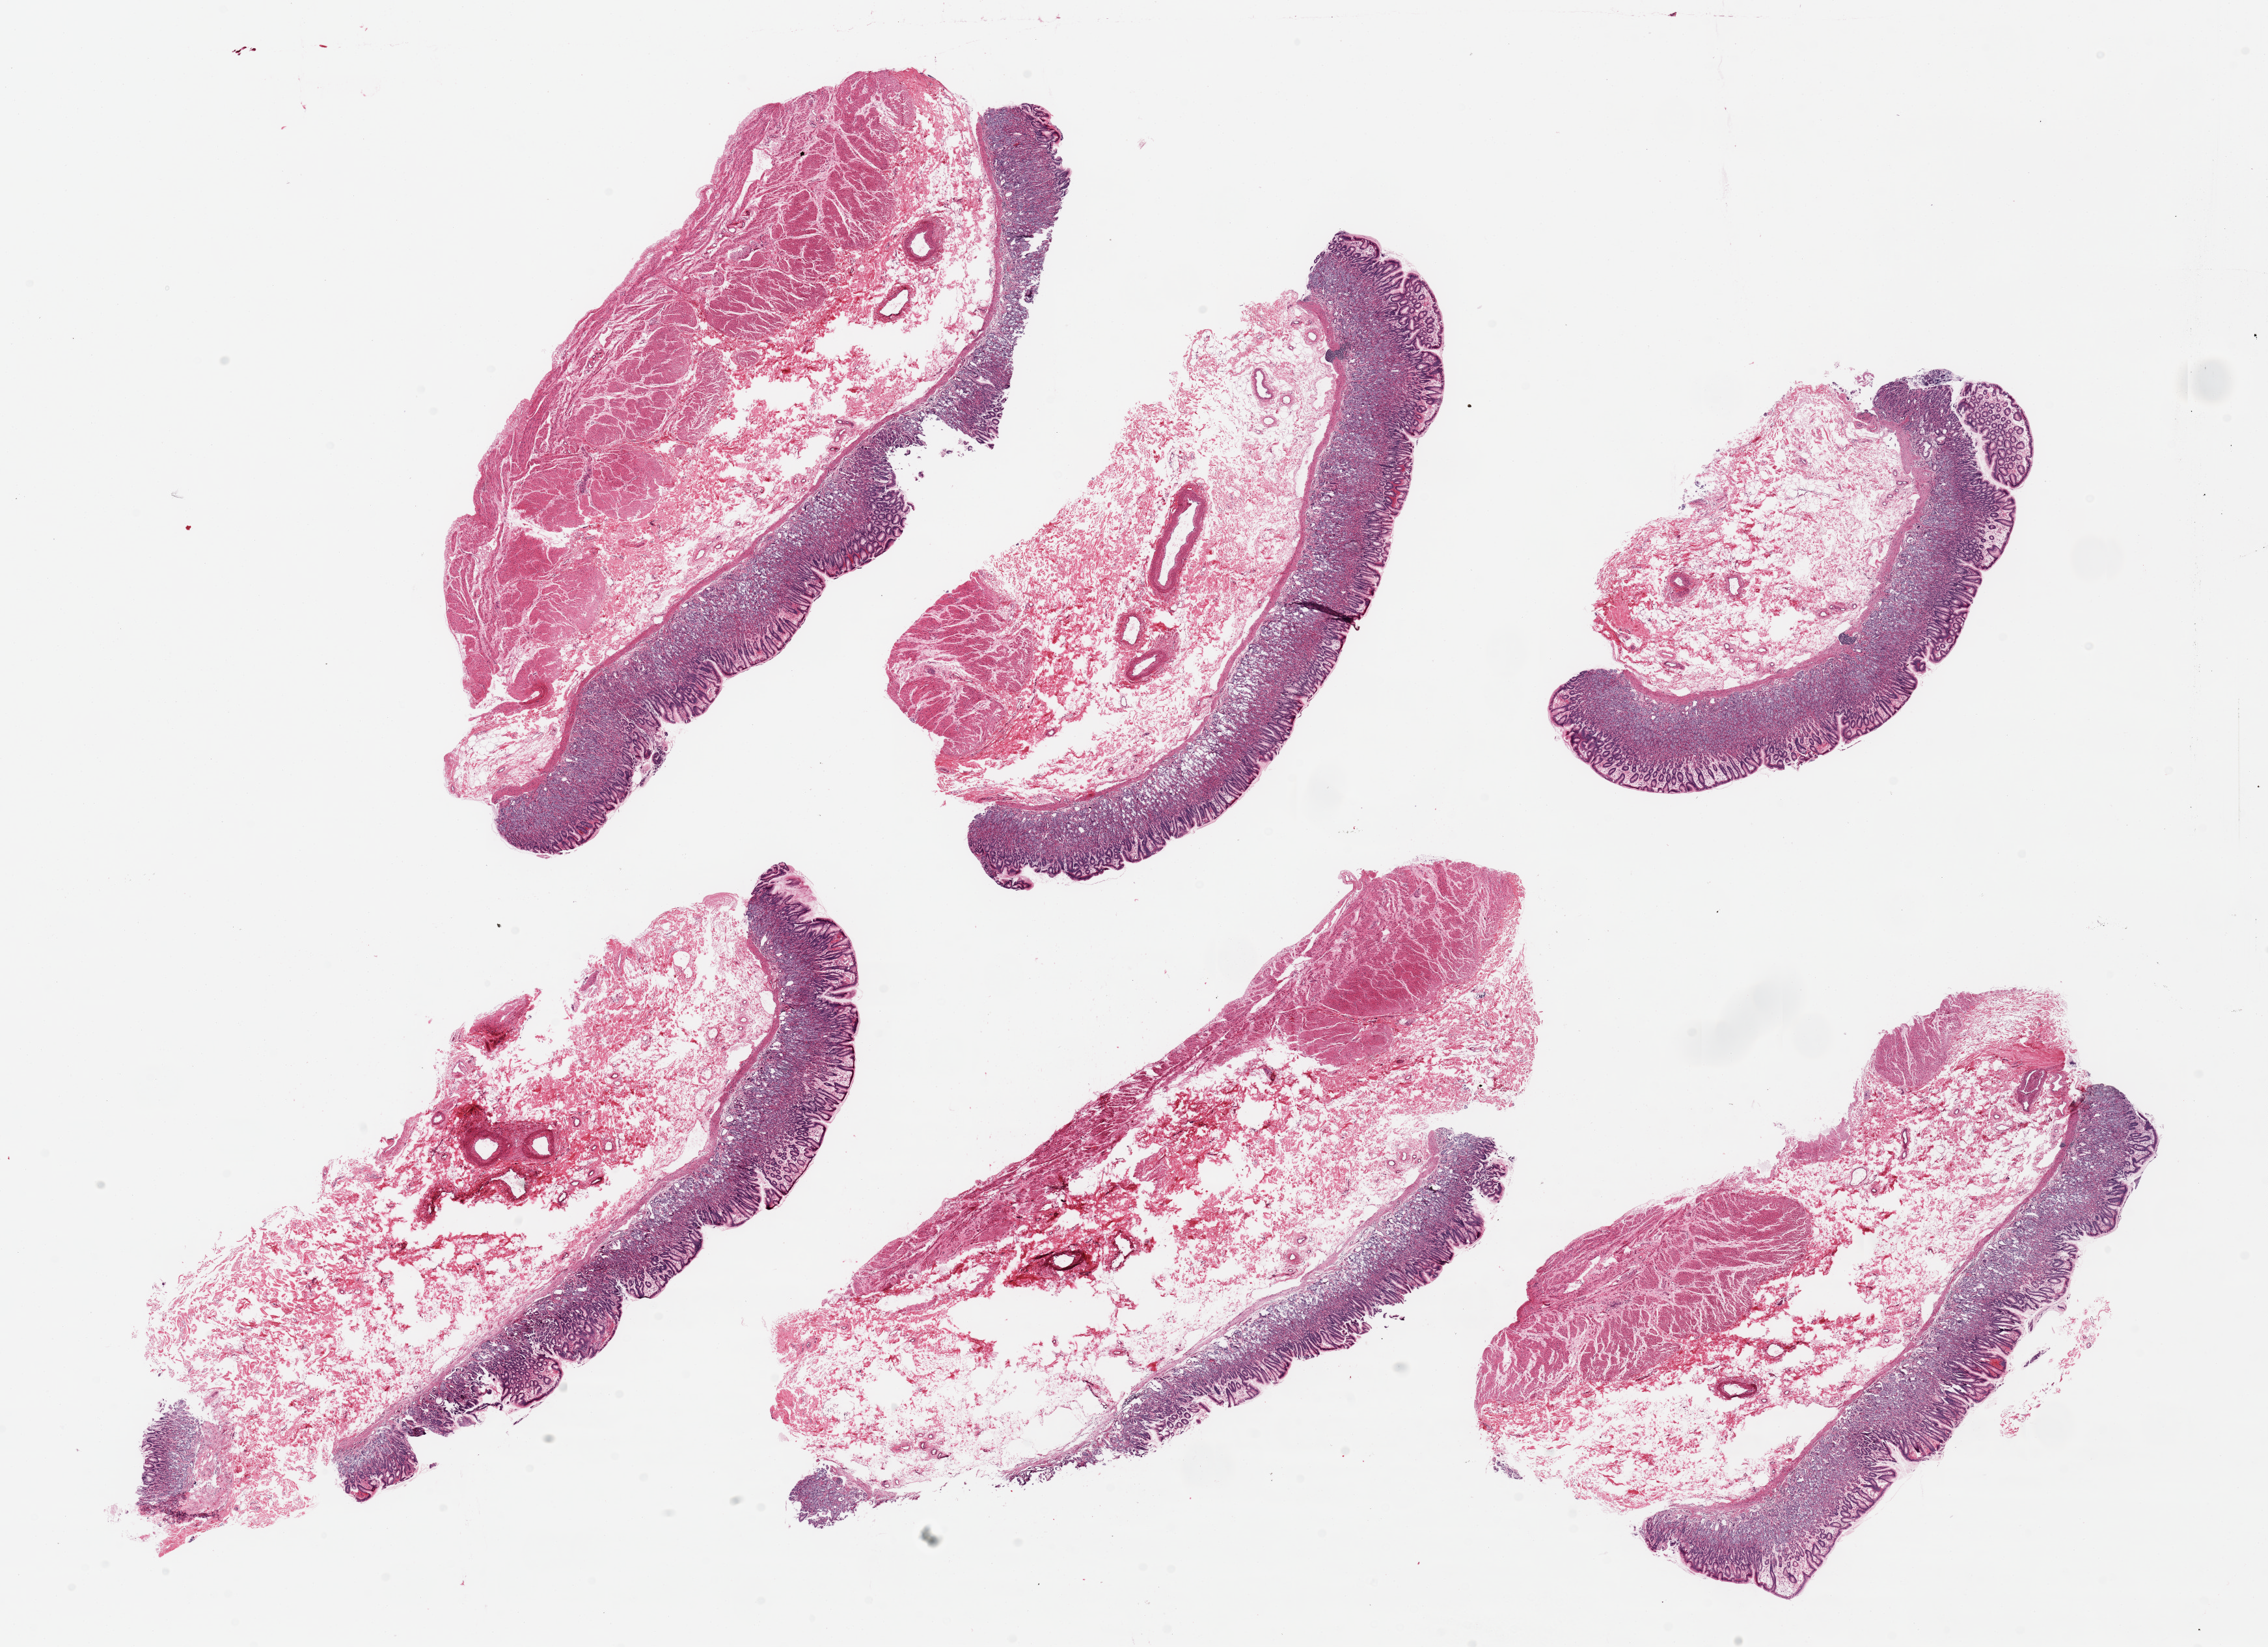
H&E whole-slide image, brightfield, a low-resolution overview of the entire scanned area, about 27.6 x 20.0 mm (slide scanned at 20x); PAXgene-fixed, paraffin-embedded tissue; target tissue: stomach; donor tissue sample. Donor: male.
Review note (as recorded): 6 pieces, mucosa well - preserved, up to ~1mm, ~25% thickness; Microcystic metaplastic changes noted.